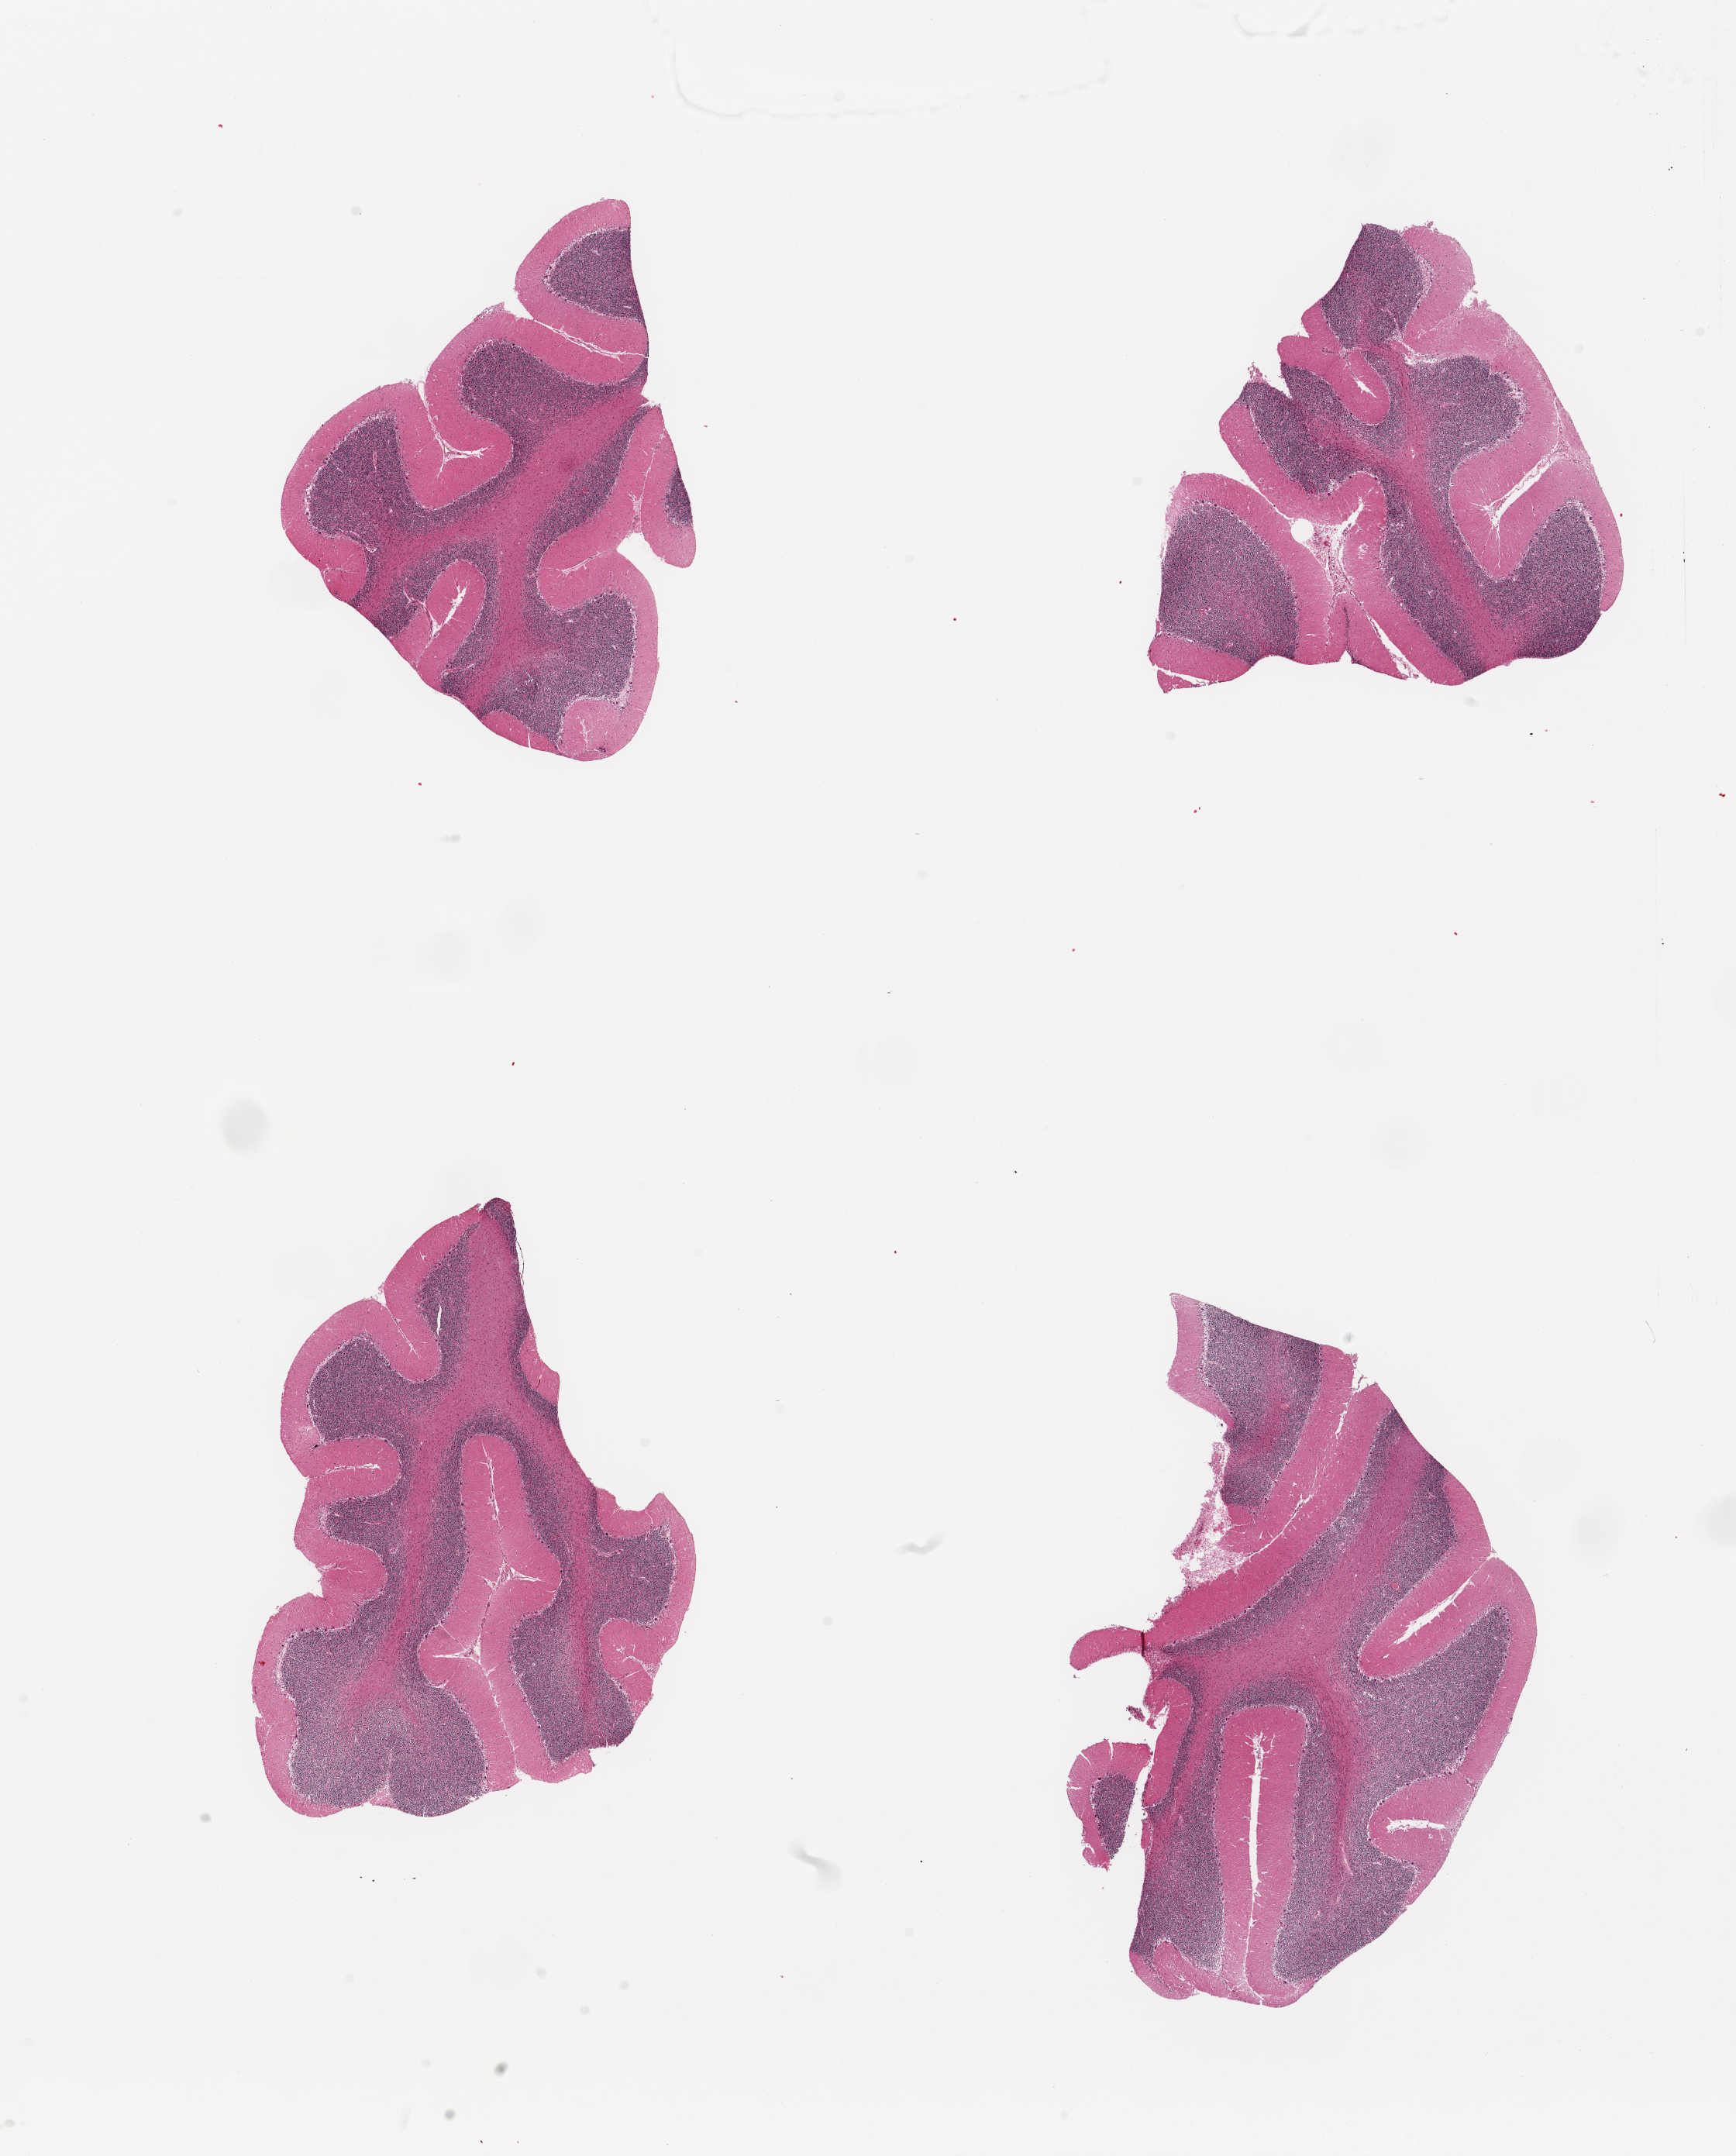
Digitized haematoxylin and eosin-stained section, whole scanned area (about 17.7 x 22.0 mm) shown as a low-resolution overview; PAXgene-fixed paraffin-embedded (PFPE) section; section of cerebellum (target tissue); donor tissue sample. Donor: male.
Reviewer comment on this tissue sample: 4 pieces, no abnormalities.